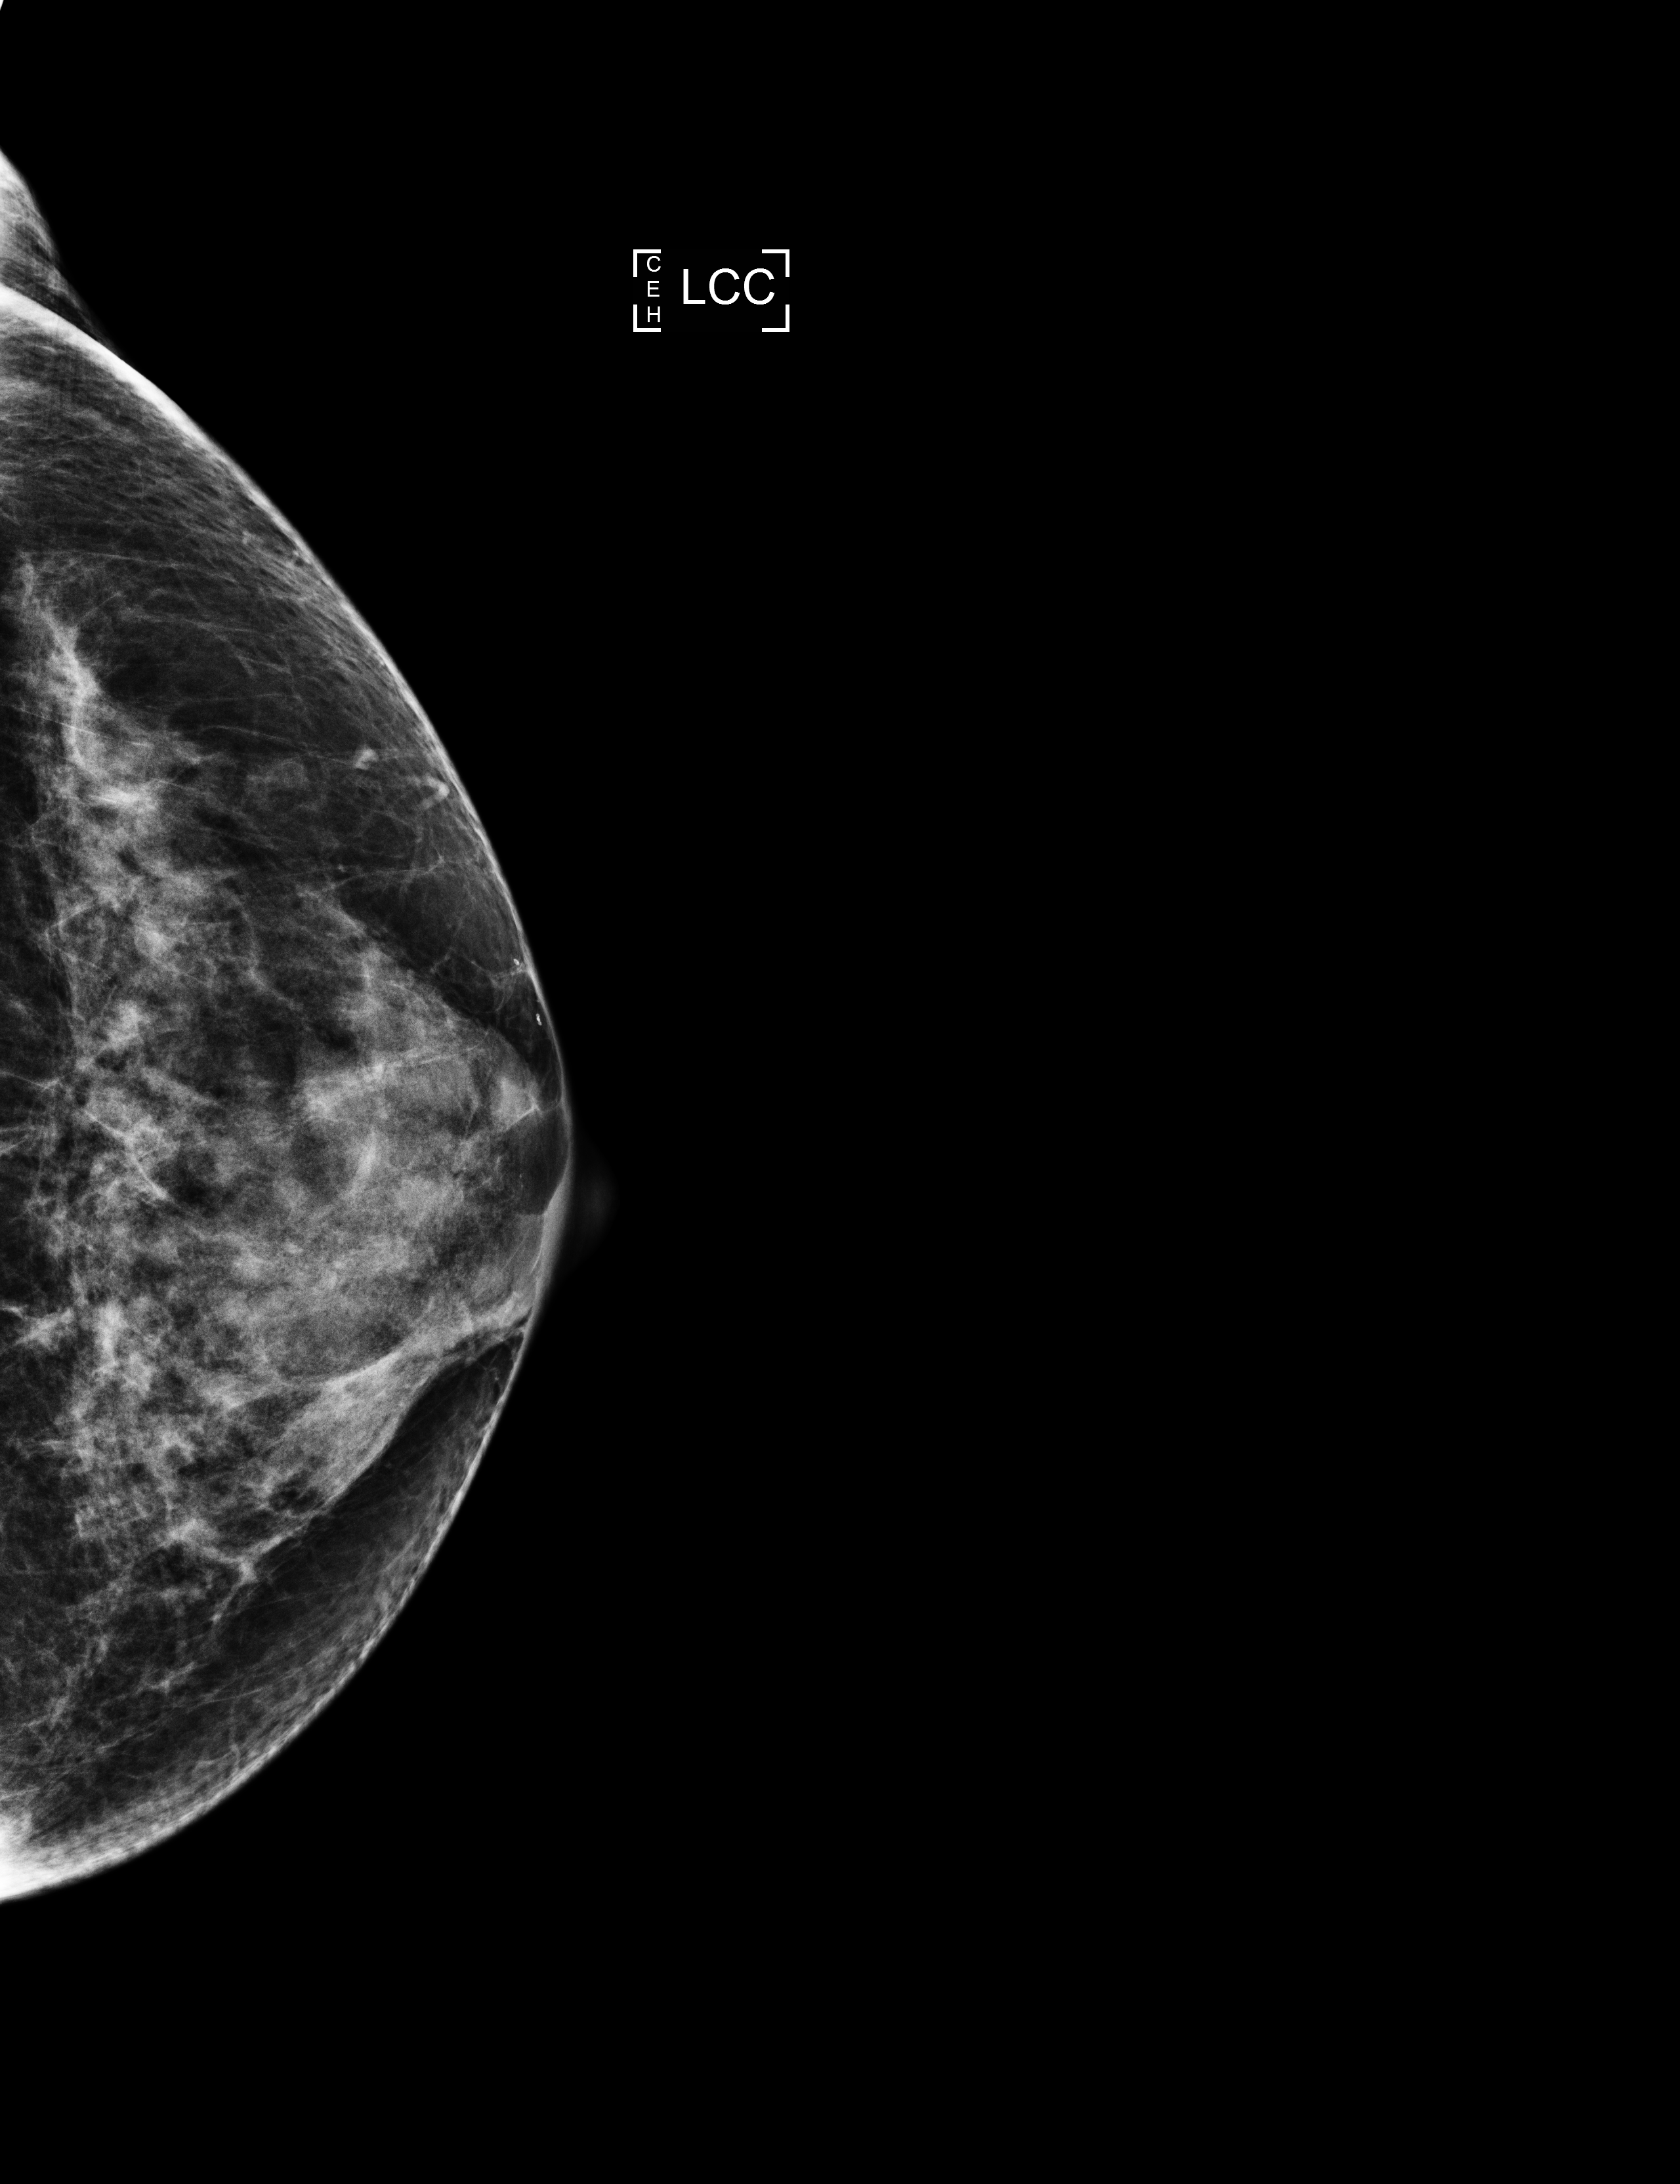
Annual screening mammography examination, compressed breast thickness 46 mm. Patient: female, 60 years.
Image type: full-field digital mammogram. Breast: left. Projection: cranio-caudal projection.